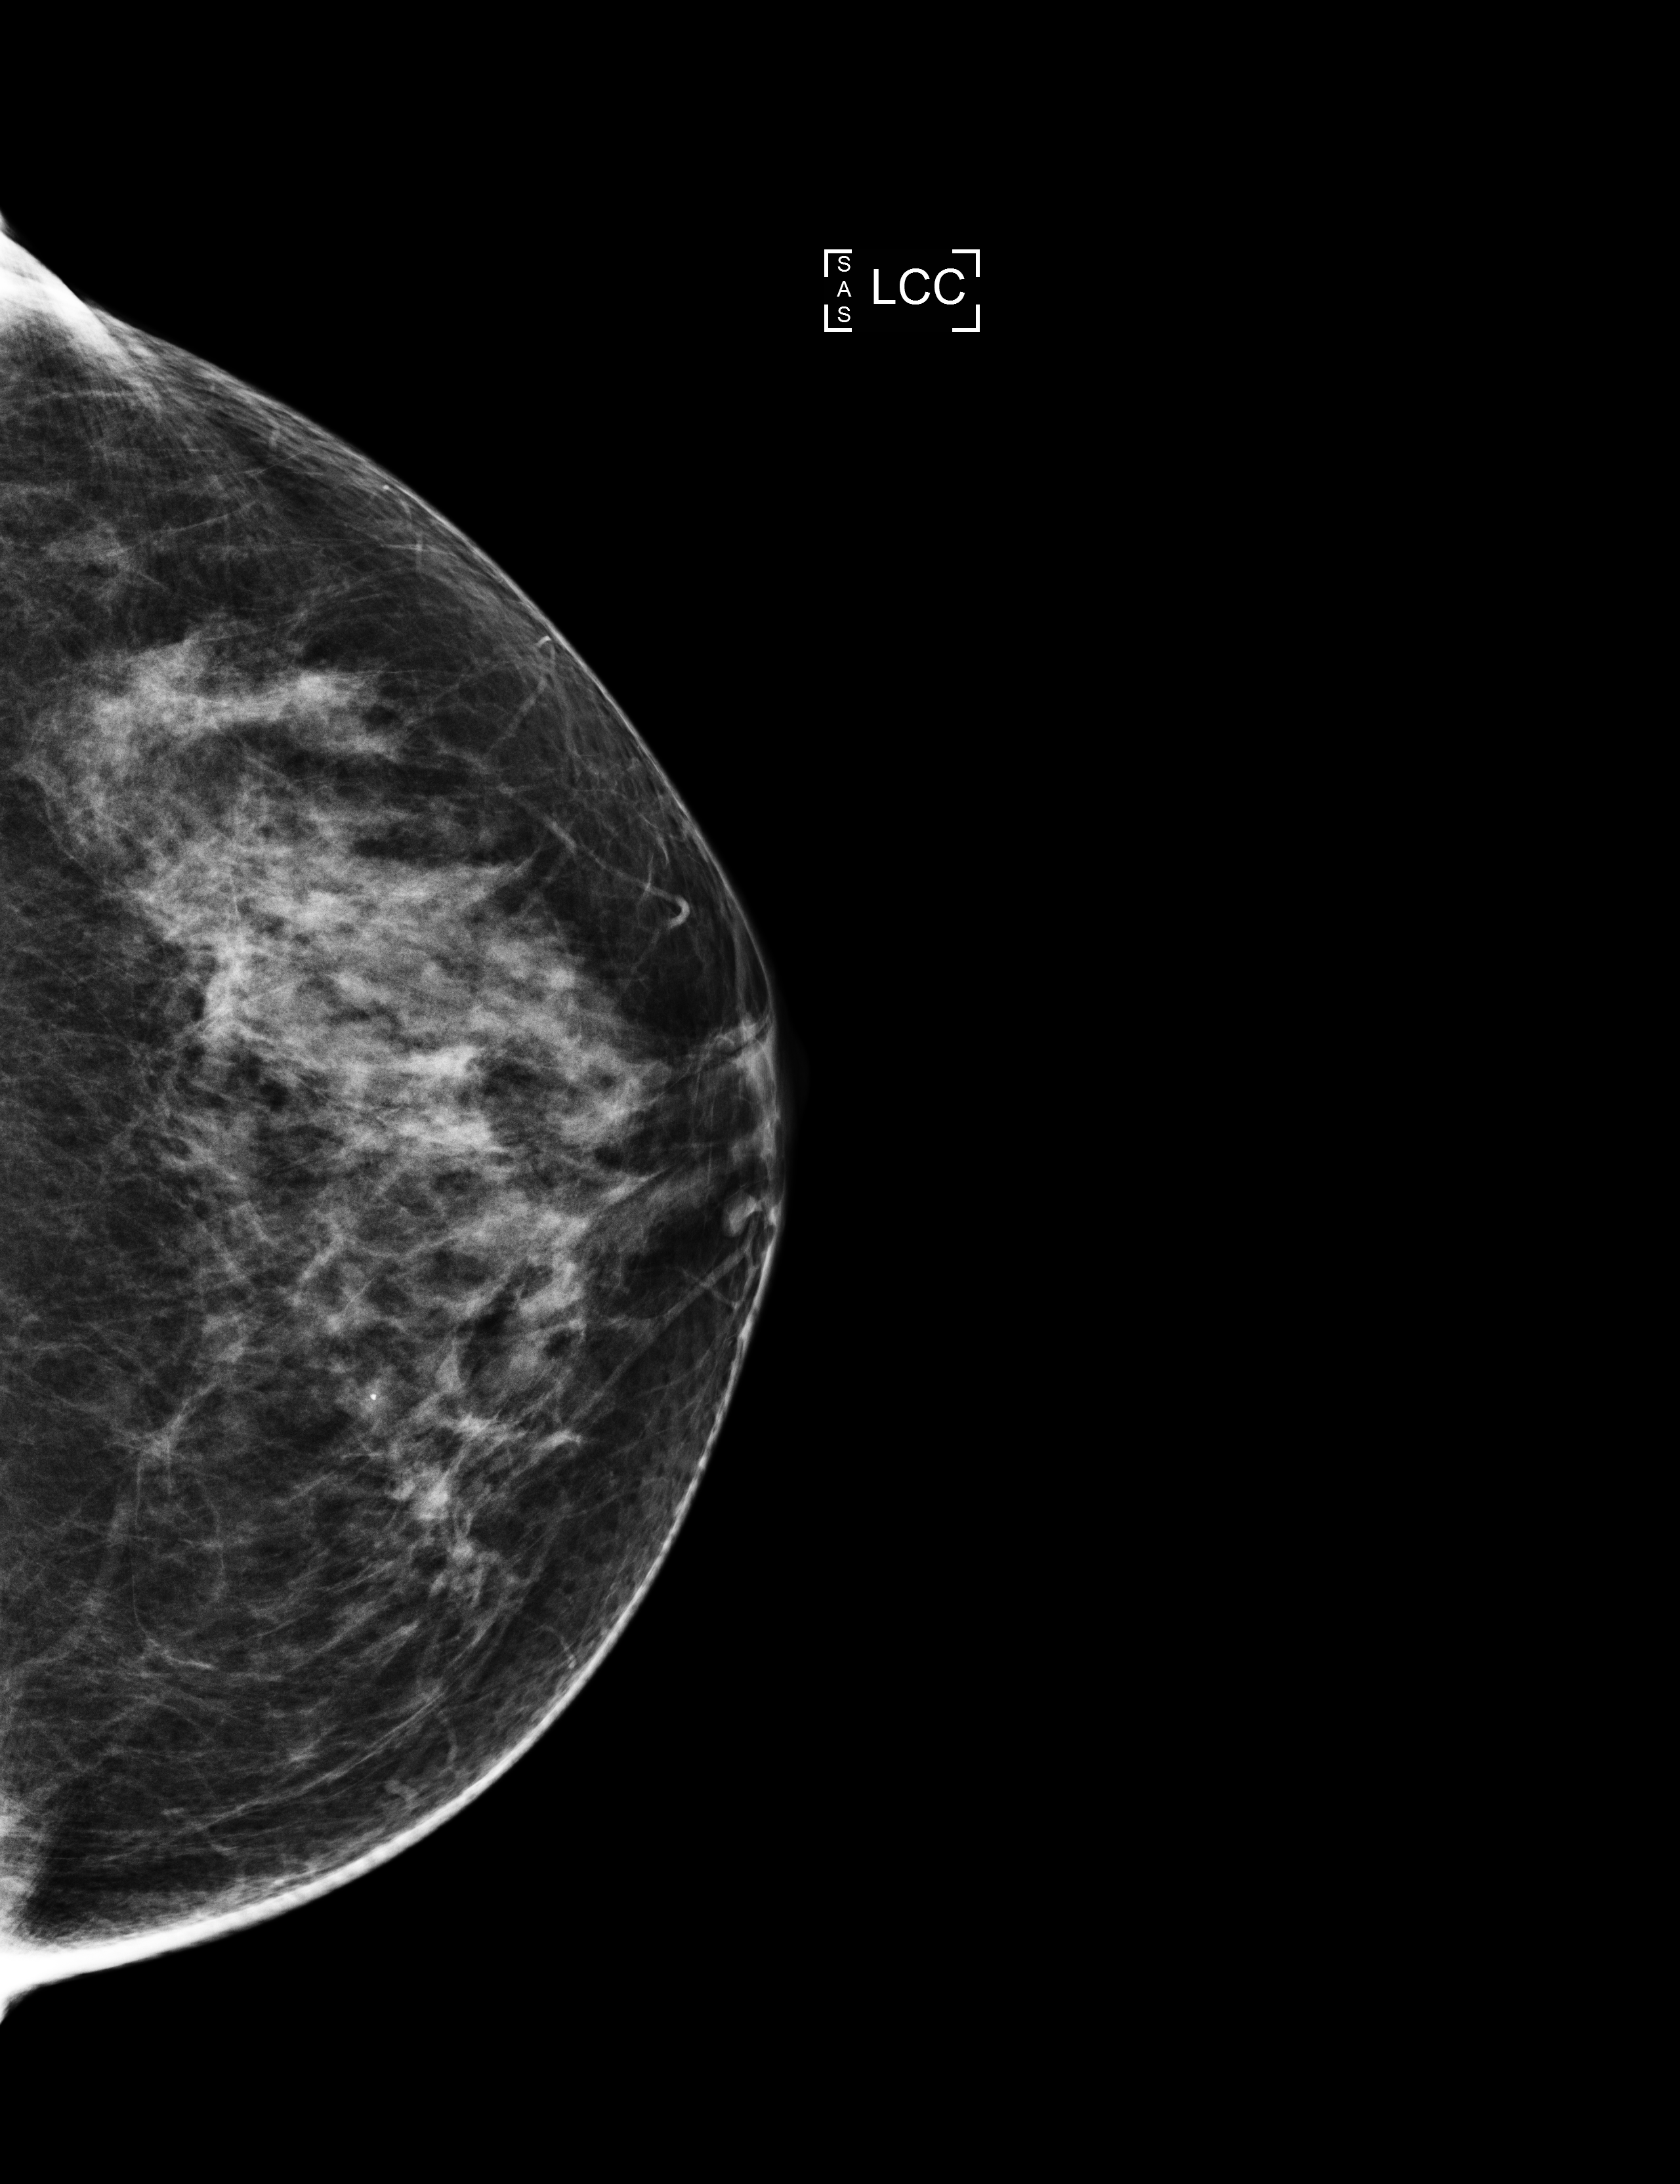
Digital mammogram (FFDM); left breast; craniocaudal (CC) view; screening examination; compressed breast thickness 62 mm. Patient: female, 54 years.
Breast density at the screening exam (both breasts): heterogeneously dense (BI-RADS density category c). Final BI-RADS assessment for this screening round (tomosynthesis exam, both breasts): category 1. Recall: no recall after this screen.